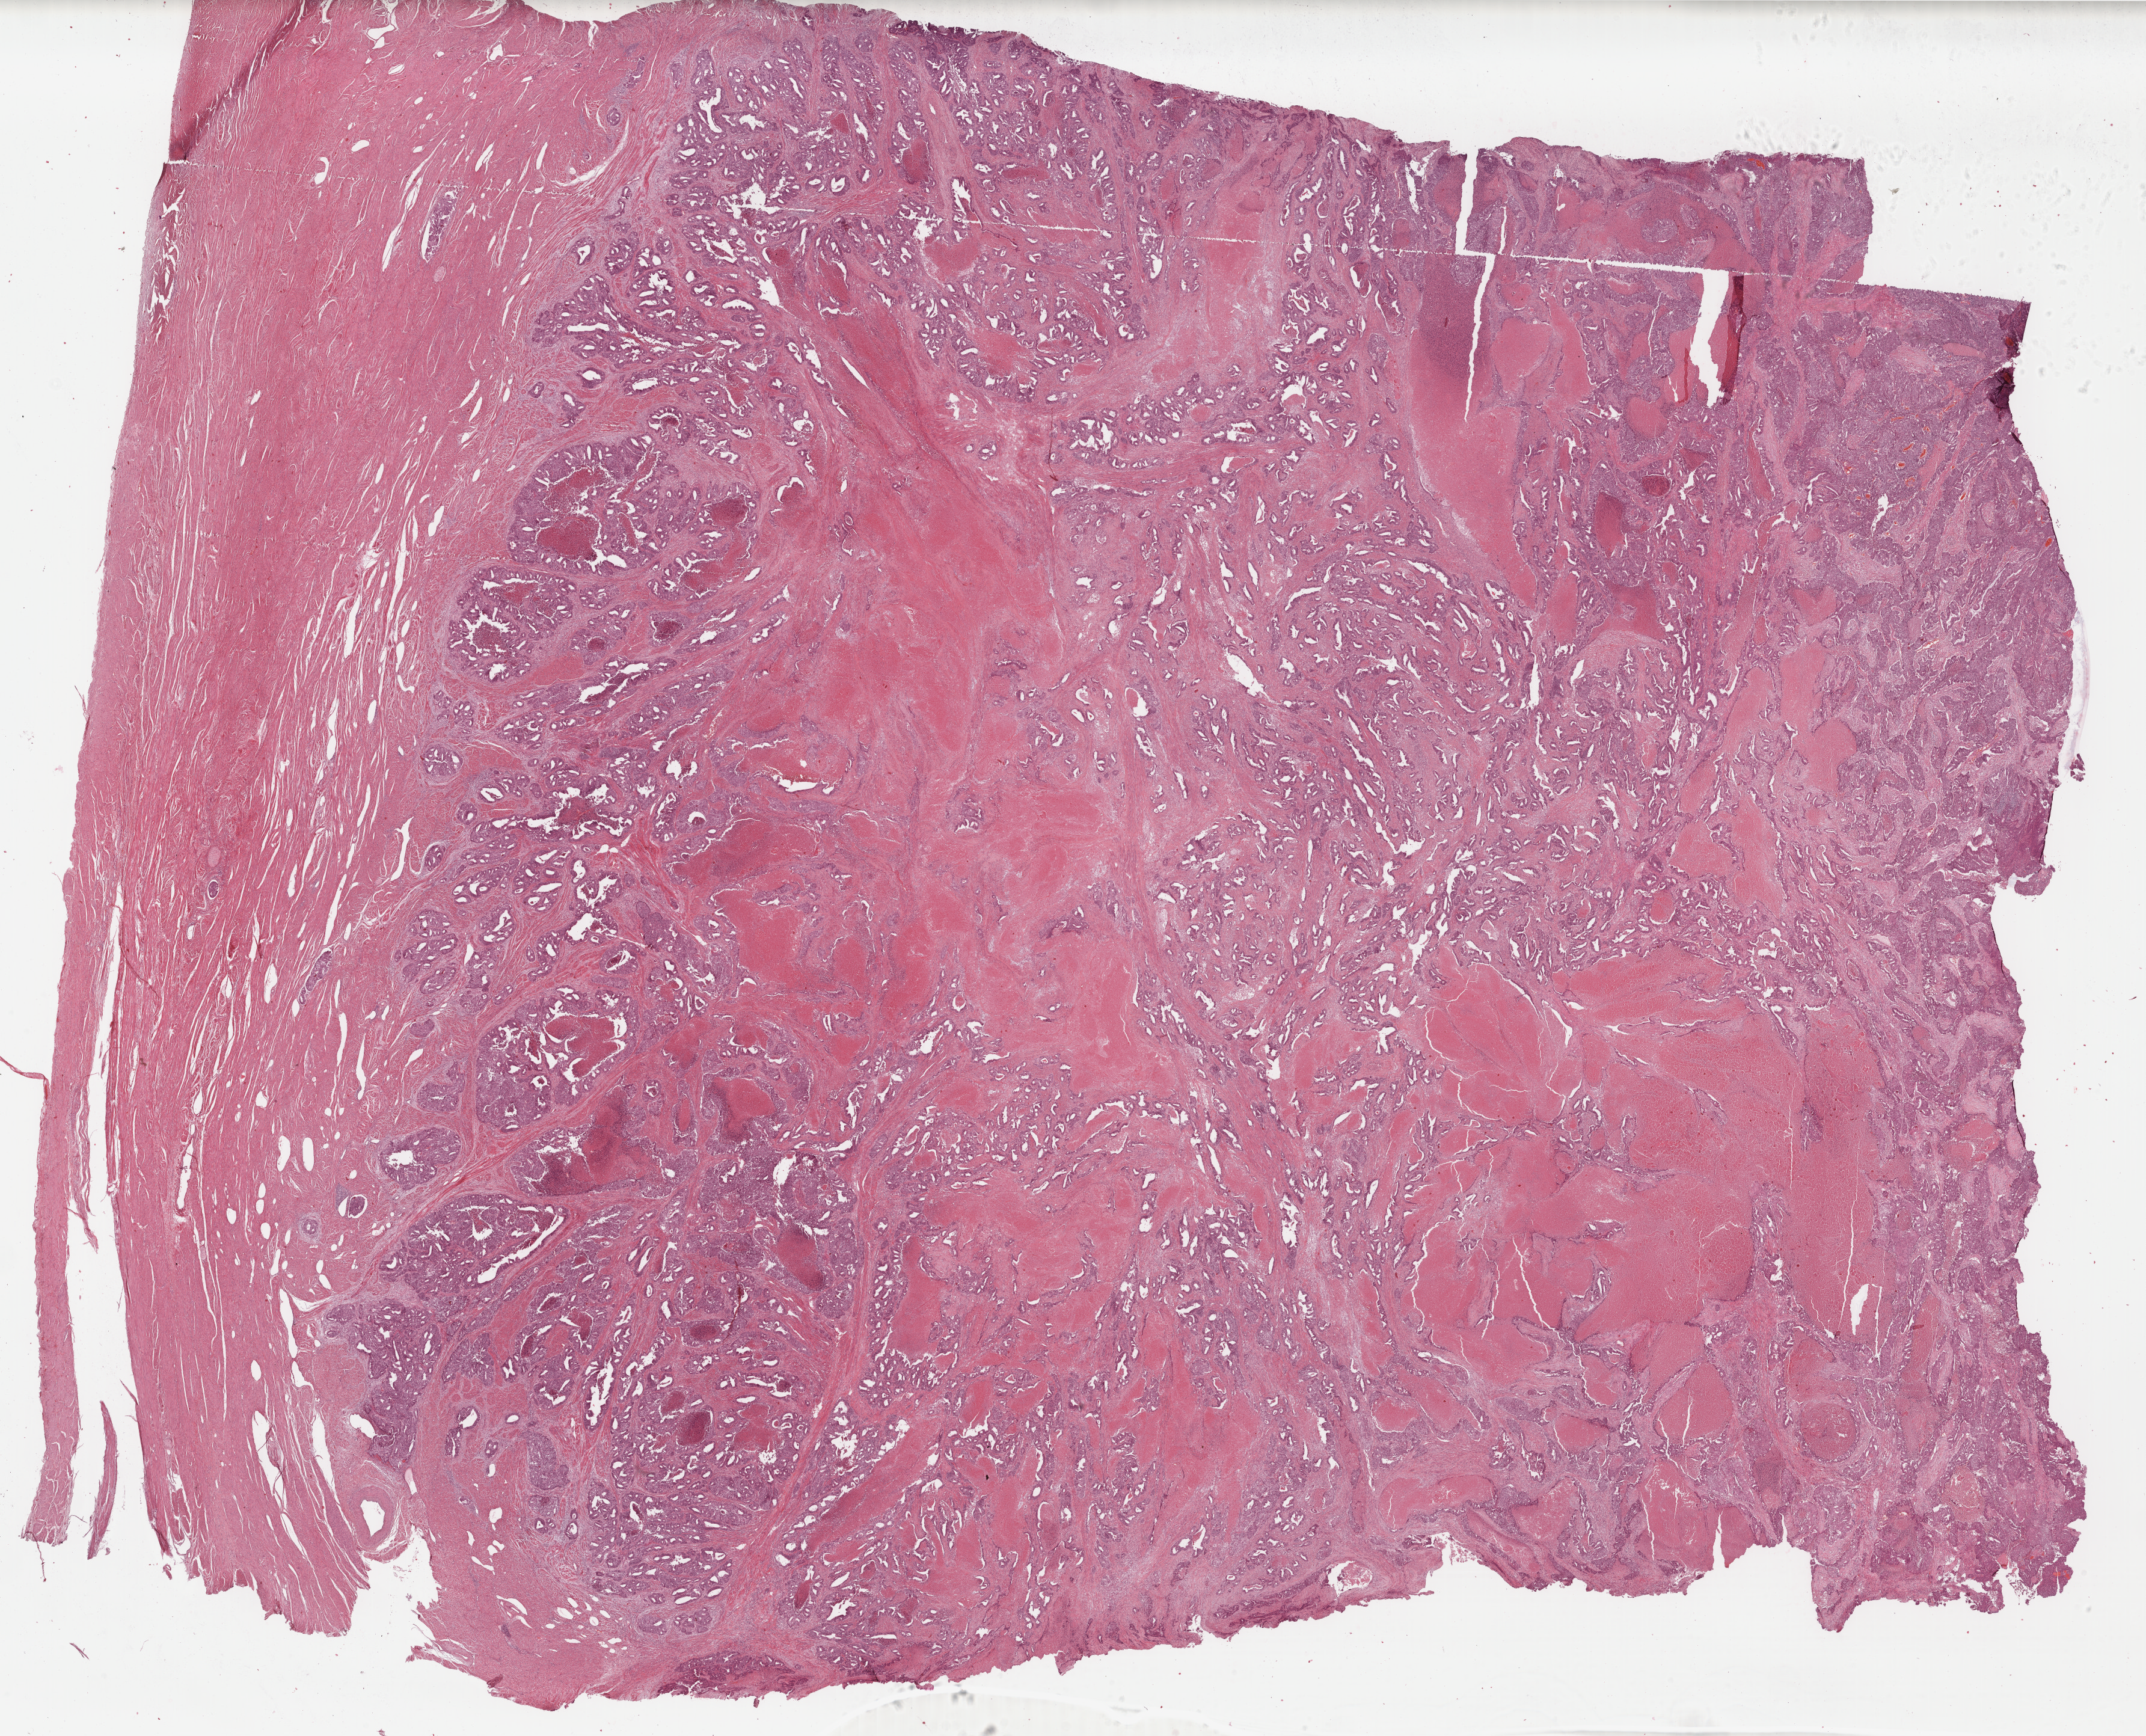
Digitized H&E-stained tissue section (whole slide), low-resolution overview of the scanned area, about 28.3 x 22.9 mm (slide scanned at 40x), formalin-fixed paraffin-embedded (FFPE) diagnostic section, uterus, primary tumour sample. Female patient; age at initial diagnosis 58 years. Histologic grade: G3 (poorly differentiated).
- FIGO stage: IIB
- histologic diagnosis: Endometrioid adenocarcinoma, NOS (endometrium)